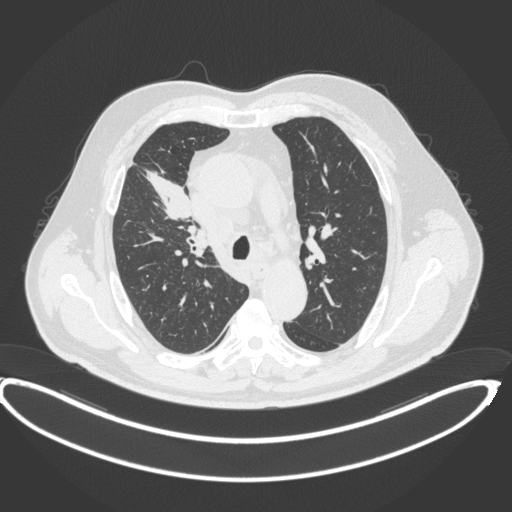
Chest CT, one axial slice. Slice 283 of 395 in the series (ordered by position). Reconstruction kernel B31f. 120 kVp. Lung window (W 1500 / L -600 HU). 512 × 512 image matrix, field of view 448 × 448 mm. Patient: male, 62 years. From the clinical record (not read from this slice): clinical TNM (as recorded): T1c N3 M1c.
Structures marked on this image (bounding box drawn by a radiologist):
- lung tumour (recorded histology: adenocarcinoma): bounding box <136,161,195,222> (left, top, right, bottom; pixels)